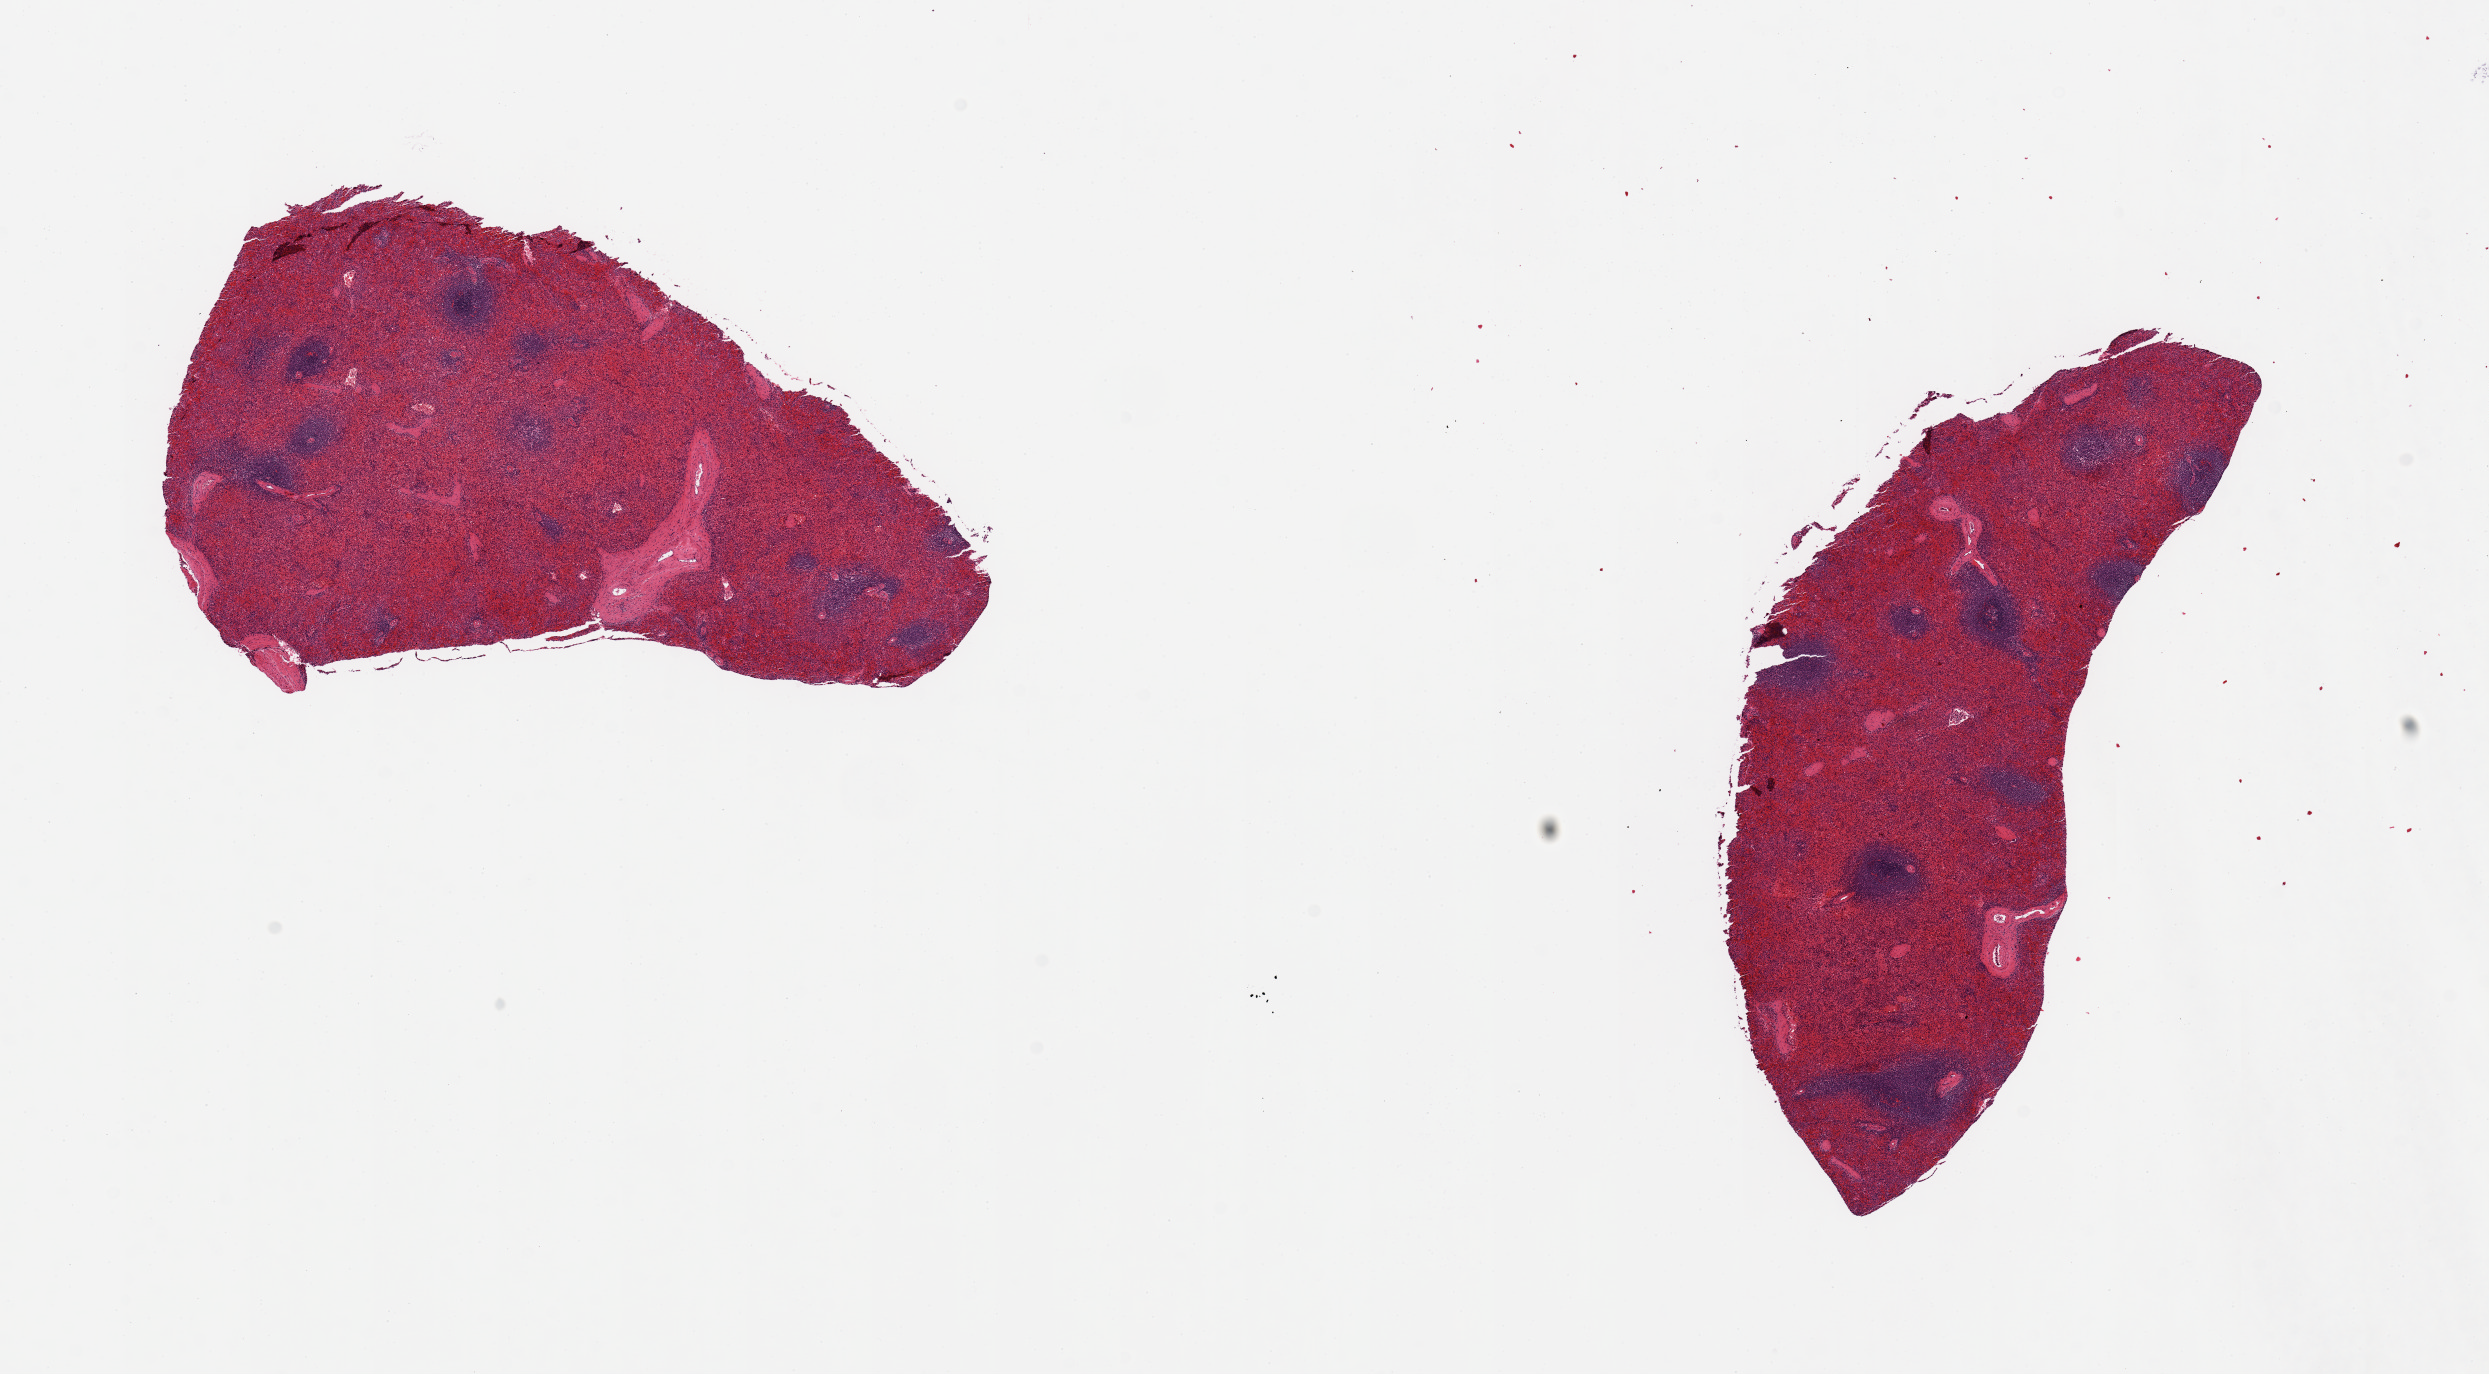
H&E whole-slide image — a low-resolution overview of the entire scanned area, about 19.7 x 10.9 mm; PAXgene-fixed paraffin-embedded (PFPE) section; section of spleen (target tissue); donor tissue sample. Donor: female.
Pathologist's review note for this sample: 2 pieces, congested.